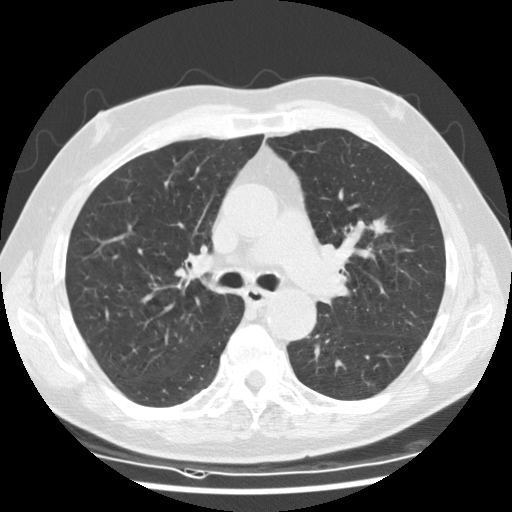
Axial slice from a low-dose chest CT screening exam. Baseline annual screen. Lung window (W 1500 / L -600 HU). Standard (soft-tissue) reconstruction kernel (STANDARD). Slice 56 of 135 in the series. Male participant, aged 73 years at enrolment. Current smoker at enrolment.
Expert reader's lesion annotation, bounding box <350,202,407,255> (left, top, right, bottom; pixels). The exam's reader record, not a measurement of the box and not confirmed to be the same lesion: non-calcified nodule or mass ≥4 mm, right lower lobe, 13 × 13 mm, smooth margins, soft tissue attenuation. Note: the box lies in the patient's left hemithorax on this image, whereas the reader's record names the right lung; they may be different findings. Official screen result: positive, change unspecified: nodule(s) >= 4 mm or enlarging nodule(s), mass(es), or other non-specific abnormalities suspicious for lung cancer. Later outcome: lung cancer diagnosed 307 days after this screen — adenocarcinoma, NOS, left upper lobe, poorly differentiated (G3), stage IA (AJCC 6th edition), 19 mm at pathology.